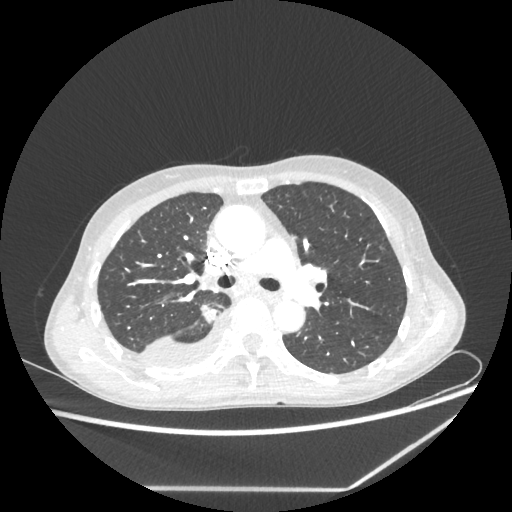
Chest CT, one axial slice. Position 146 of 237 along the scan axis. Reconstruction kernel STANDARD. 80 kVp. Lung window (W 1500 / L -600 HU). 1.25 mm slice thickness. 512 × 512 image matrix, field of view 364 × 364 mm. Patient: female, 59 years. From the clinical record (not read from this slice): clinical TNM (as recorded): T1c N1 M1.
Annotated regions visible in this slice (rectangle marked by the reading radiologist):
- lung tumour (recorded histology: adenocarcinoma): bounding box (x1, y1, x2, y2) in pixels: (200, 305, 220, 327)